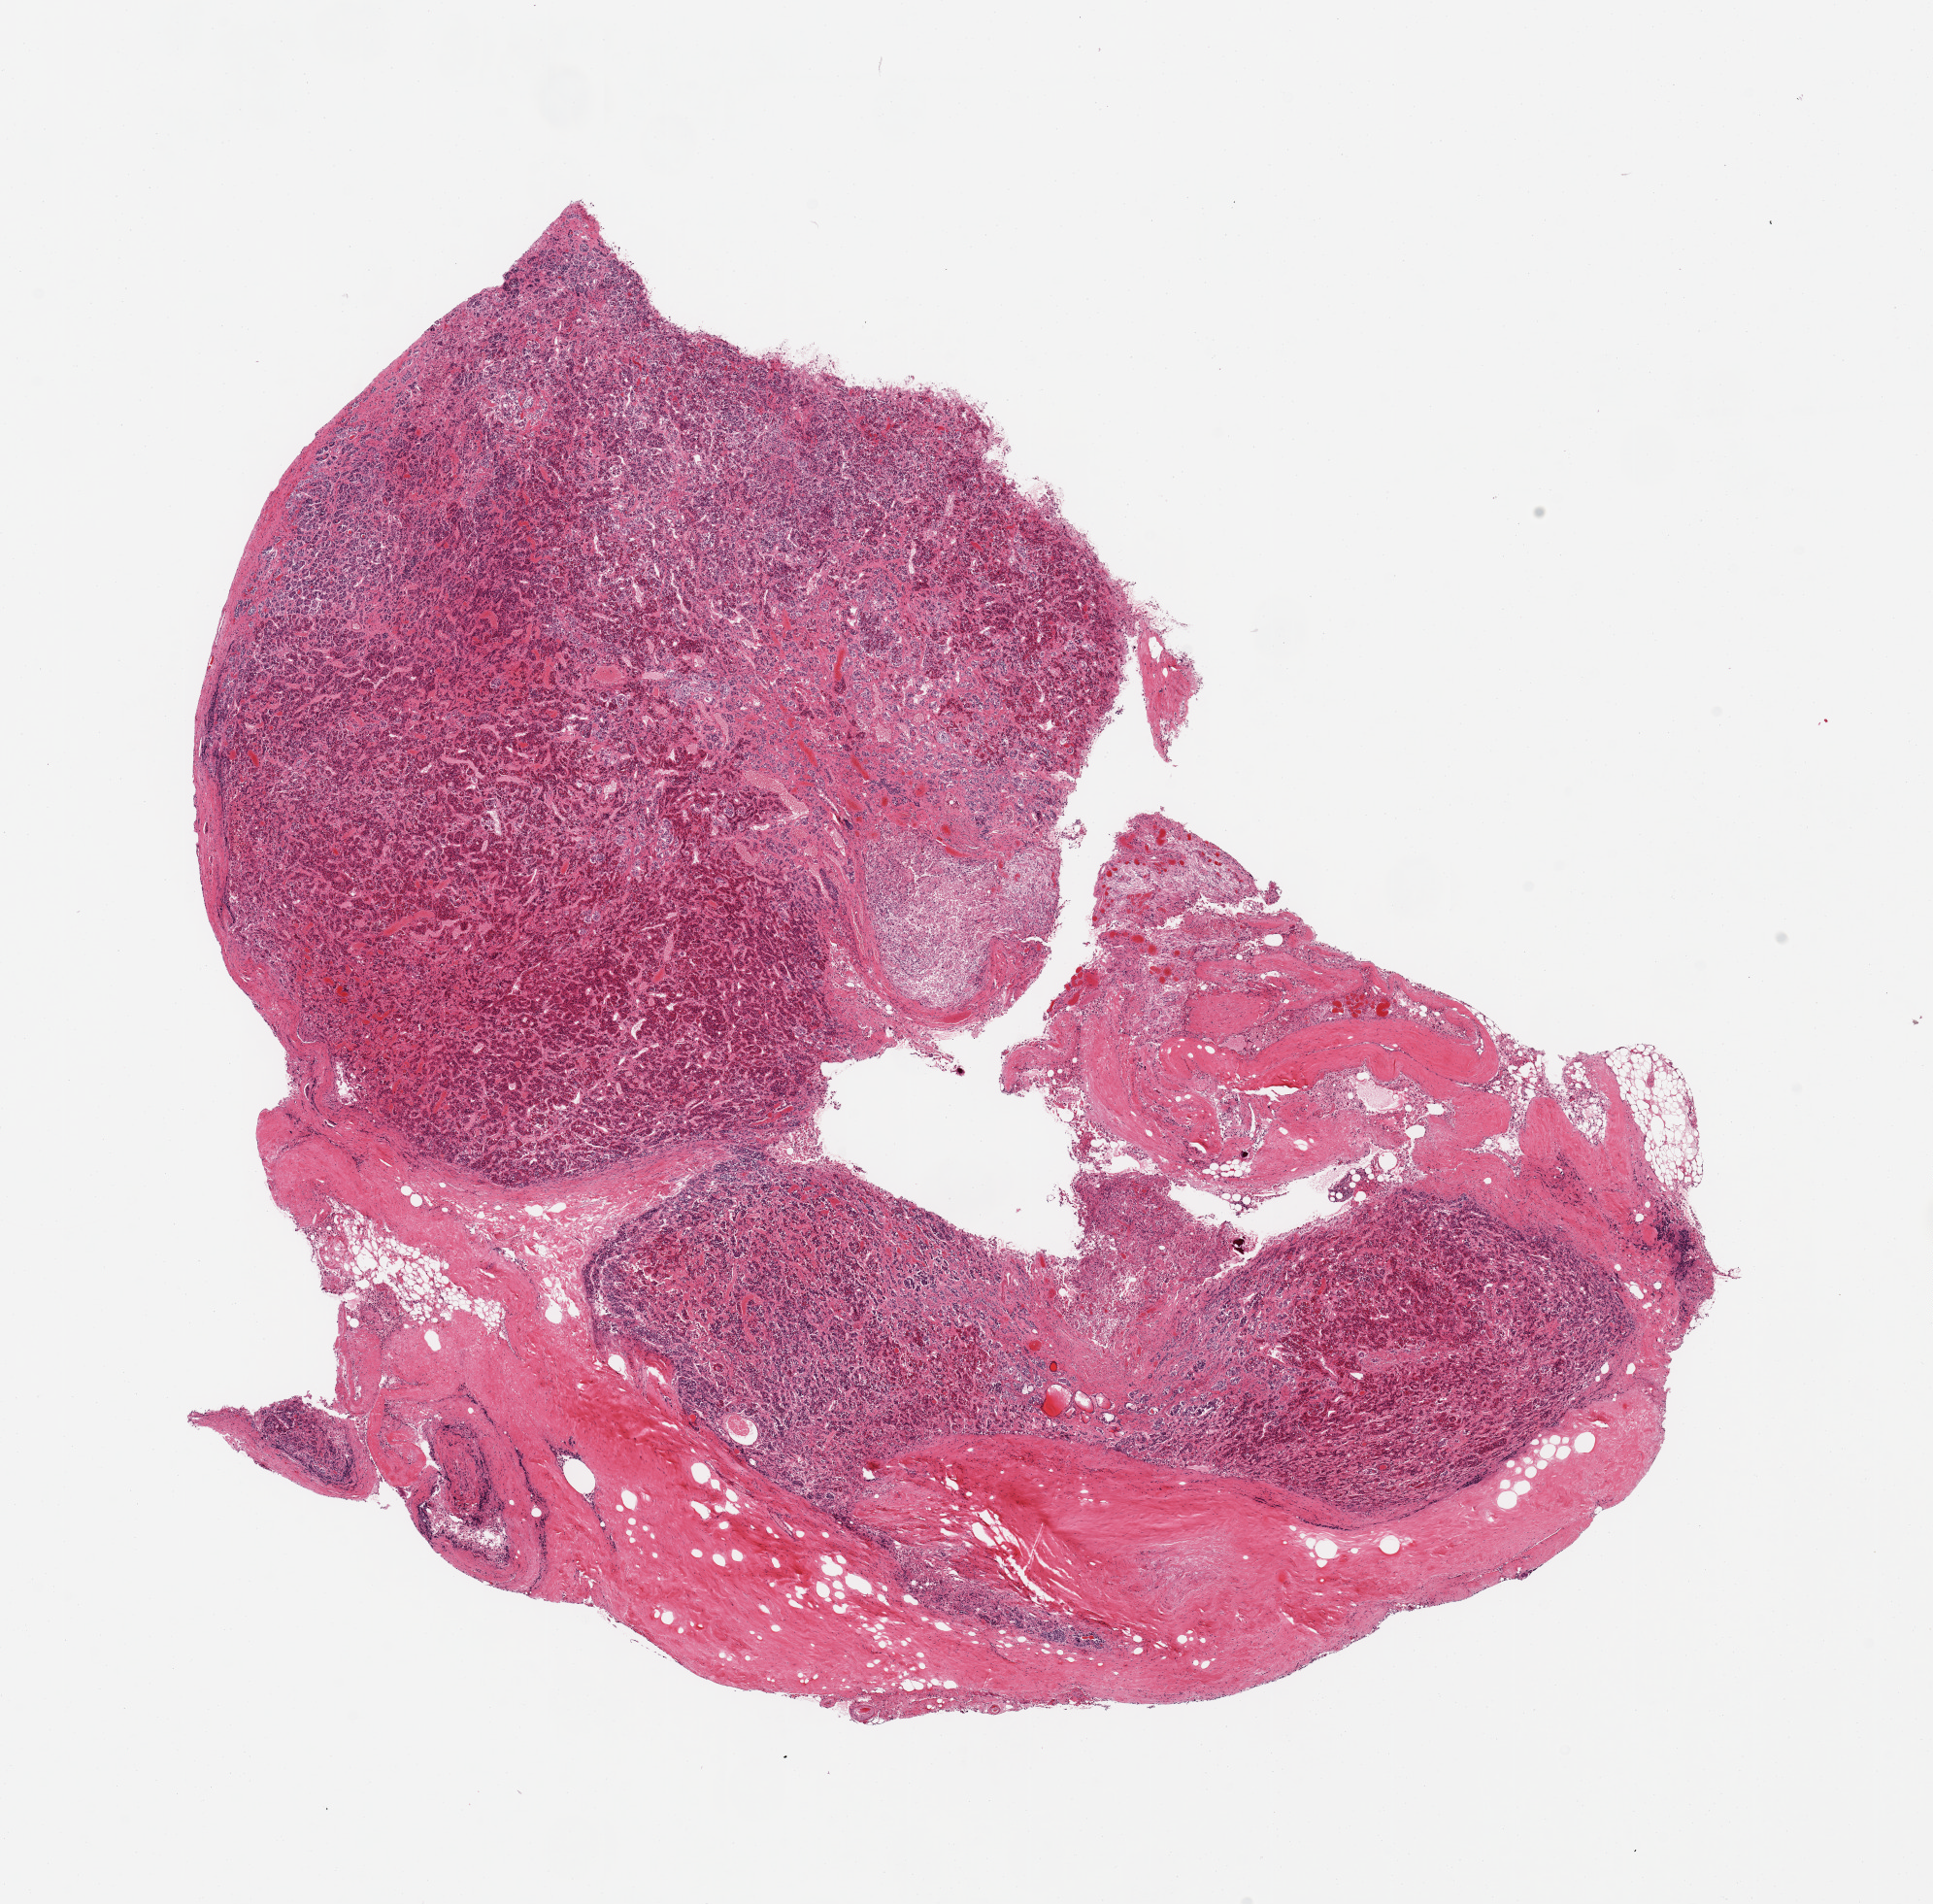
Whole-slide image, haematoxylin and eosin stain, whole scanned area (about 15.8 x 15.5 mm) shown as a low-resolution overview; PAXgene-fixed paraffin-embedded (PFPE) section; sampled site (target tissue): pituitary; donor tissue sample.
Reviewer comment on this tissue sample: 1 piece; mostly adenohypophysis; small neurohypophysis component; congestion.